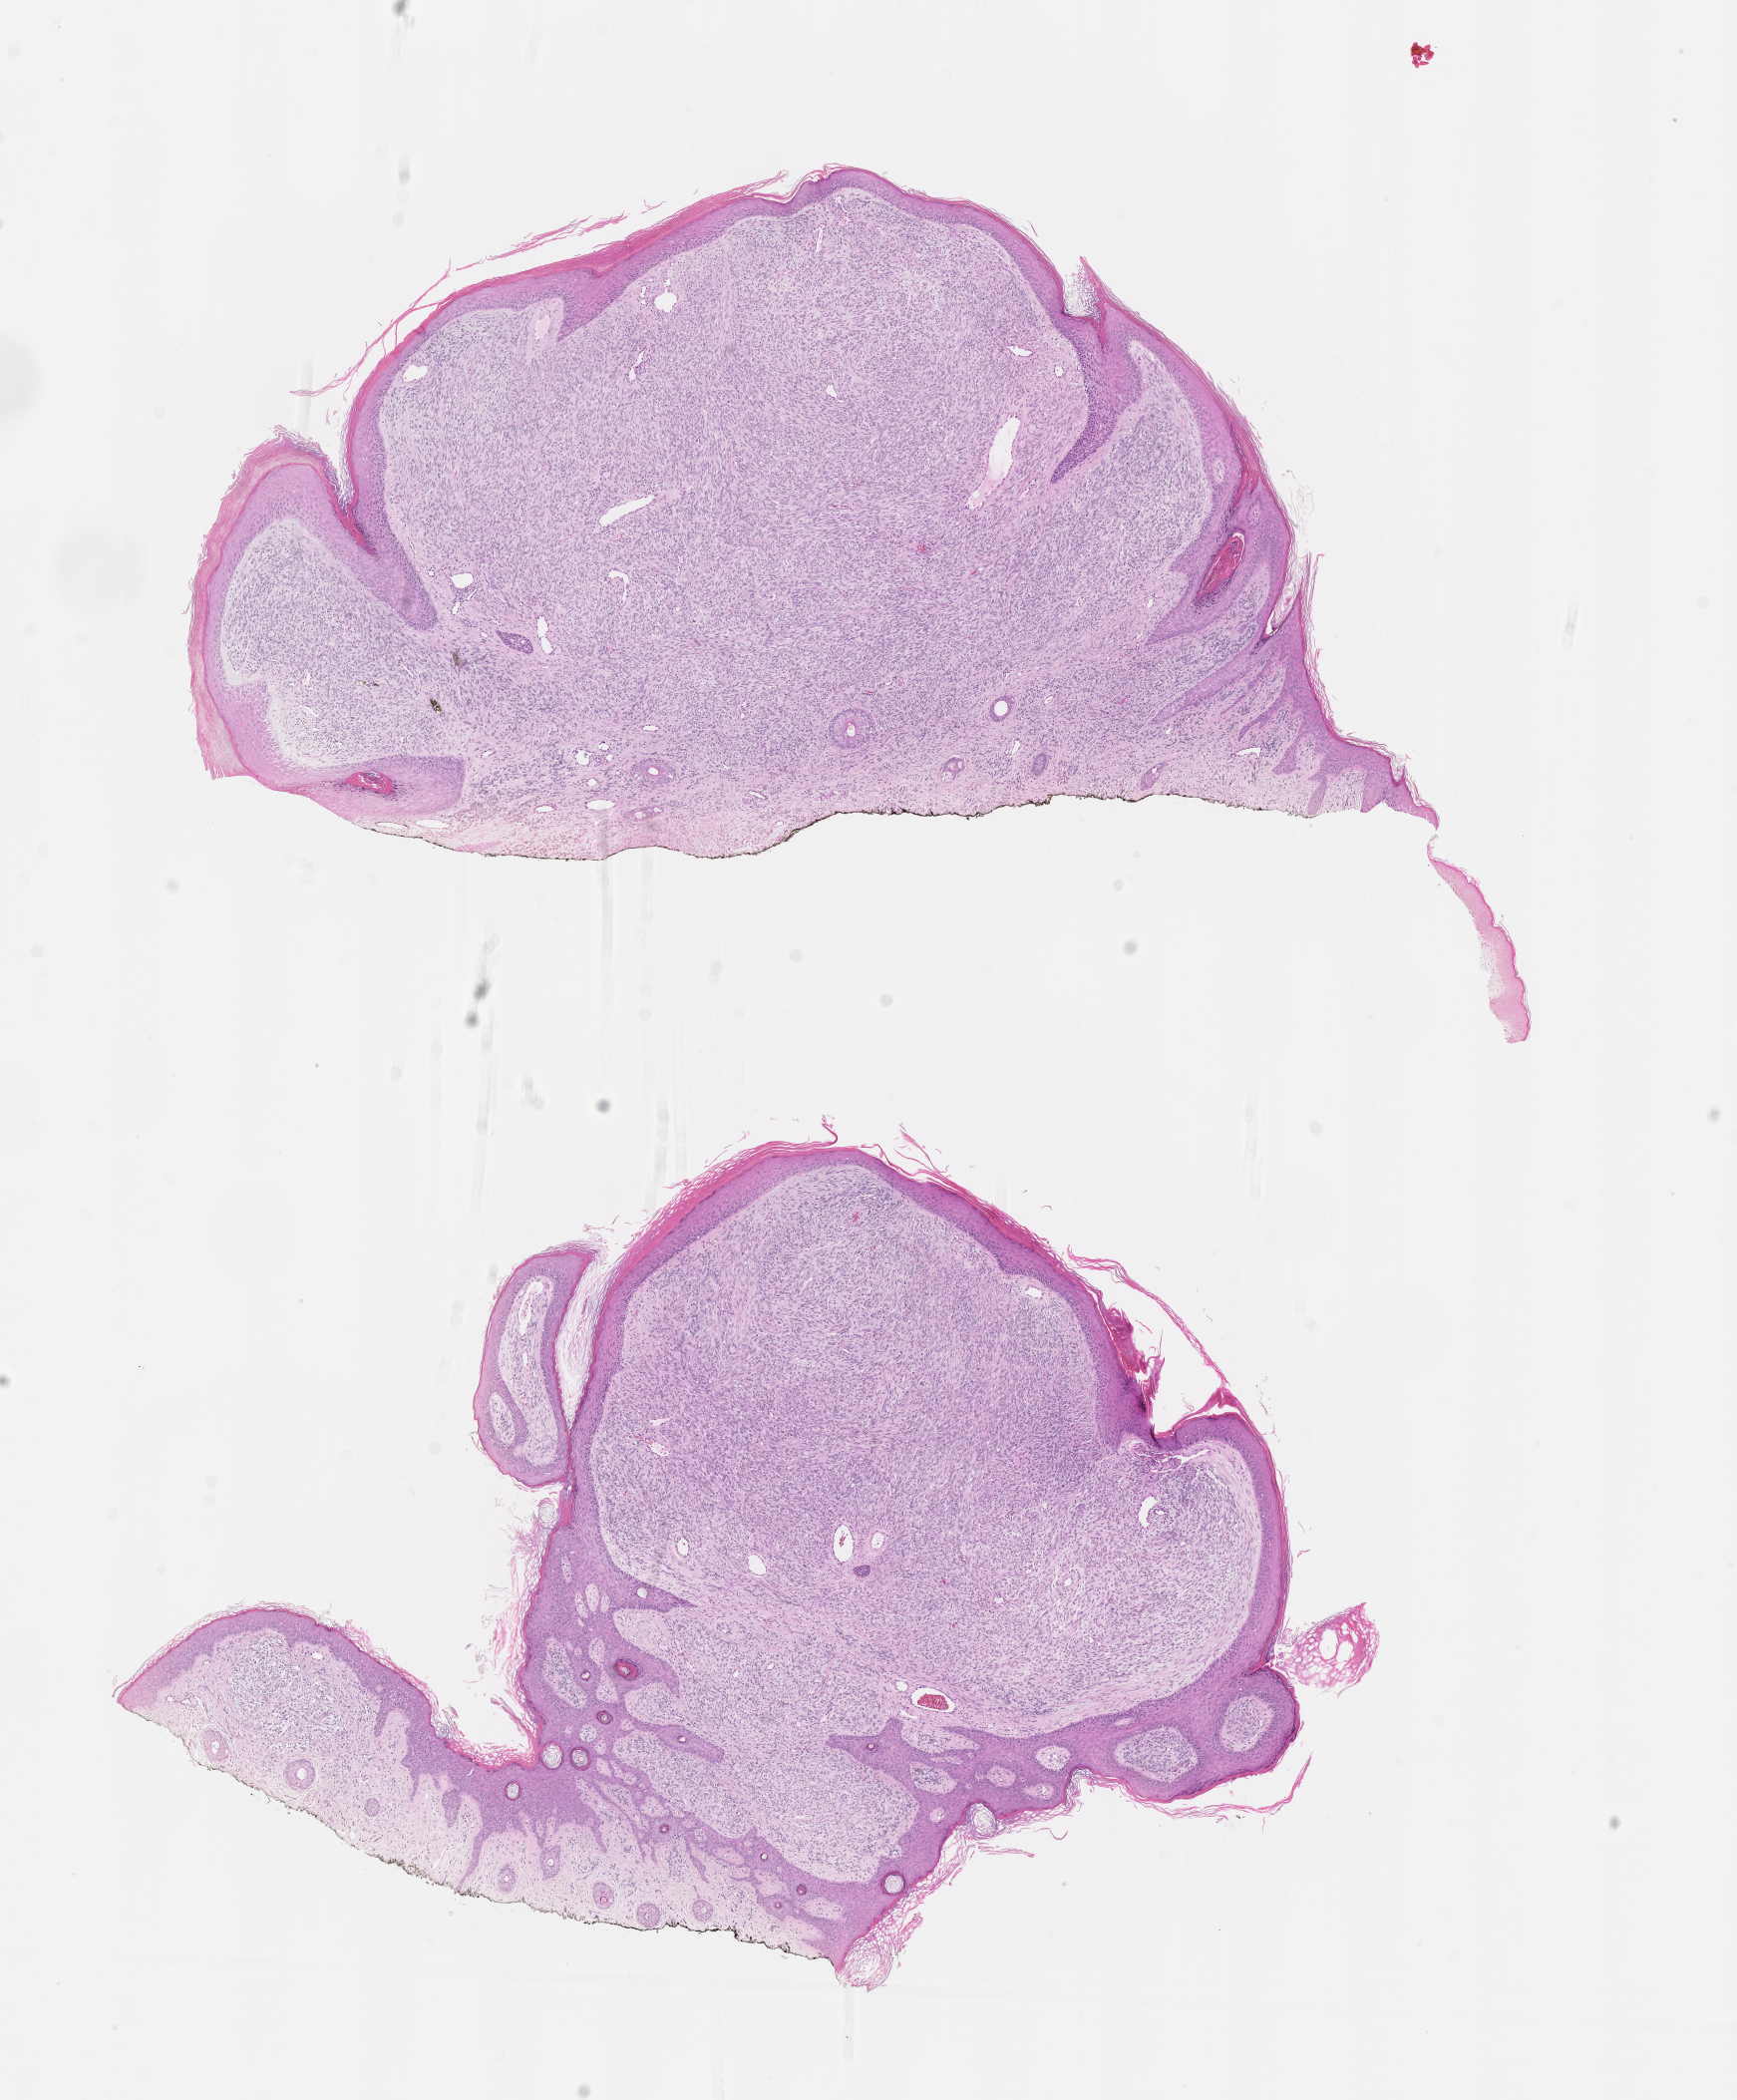
Hematoxylin and eosin (H&E) whole-slide image of tumor tissue — whole scanned area (about 7.0 x 8.5 mm) shown as a low-resolution overview. Formalin-fixed paraffin-embedded section. Female patient, age at diagnosis 3.8 years.
Diagnosis: rhabdomyosarcoma; histological classification: spindle cell rhabdomyosarcoma. Metastatic status at presentation (as recorded): non-metastatic. Stage (as recorded): 1.